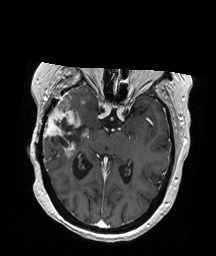
Brain MRI from a brain-tumour surgery series, one axial slice. Slice 112 of 192 in the series (ordered by position). T1-weighted post-contrast. 1 mm slice thickness. 216 × 256 image matrix, field of view 211 × 250 mm. From the clinical record (not read from this slice): histopathology: Glioblastoma; WHO grade: 4; IDH mutation: no; tumour location: Right Temporal.
Outlined on this slice (outlined manually by an expert reader):
- tumour: bounding box [x1, y1, x2, y2] px = [43, 93, 91, 158]